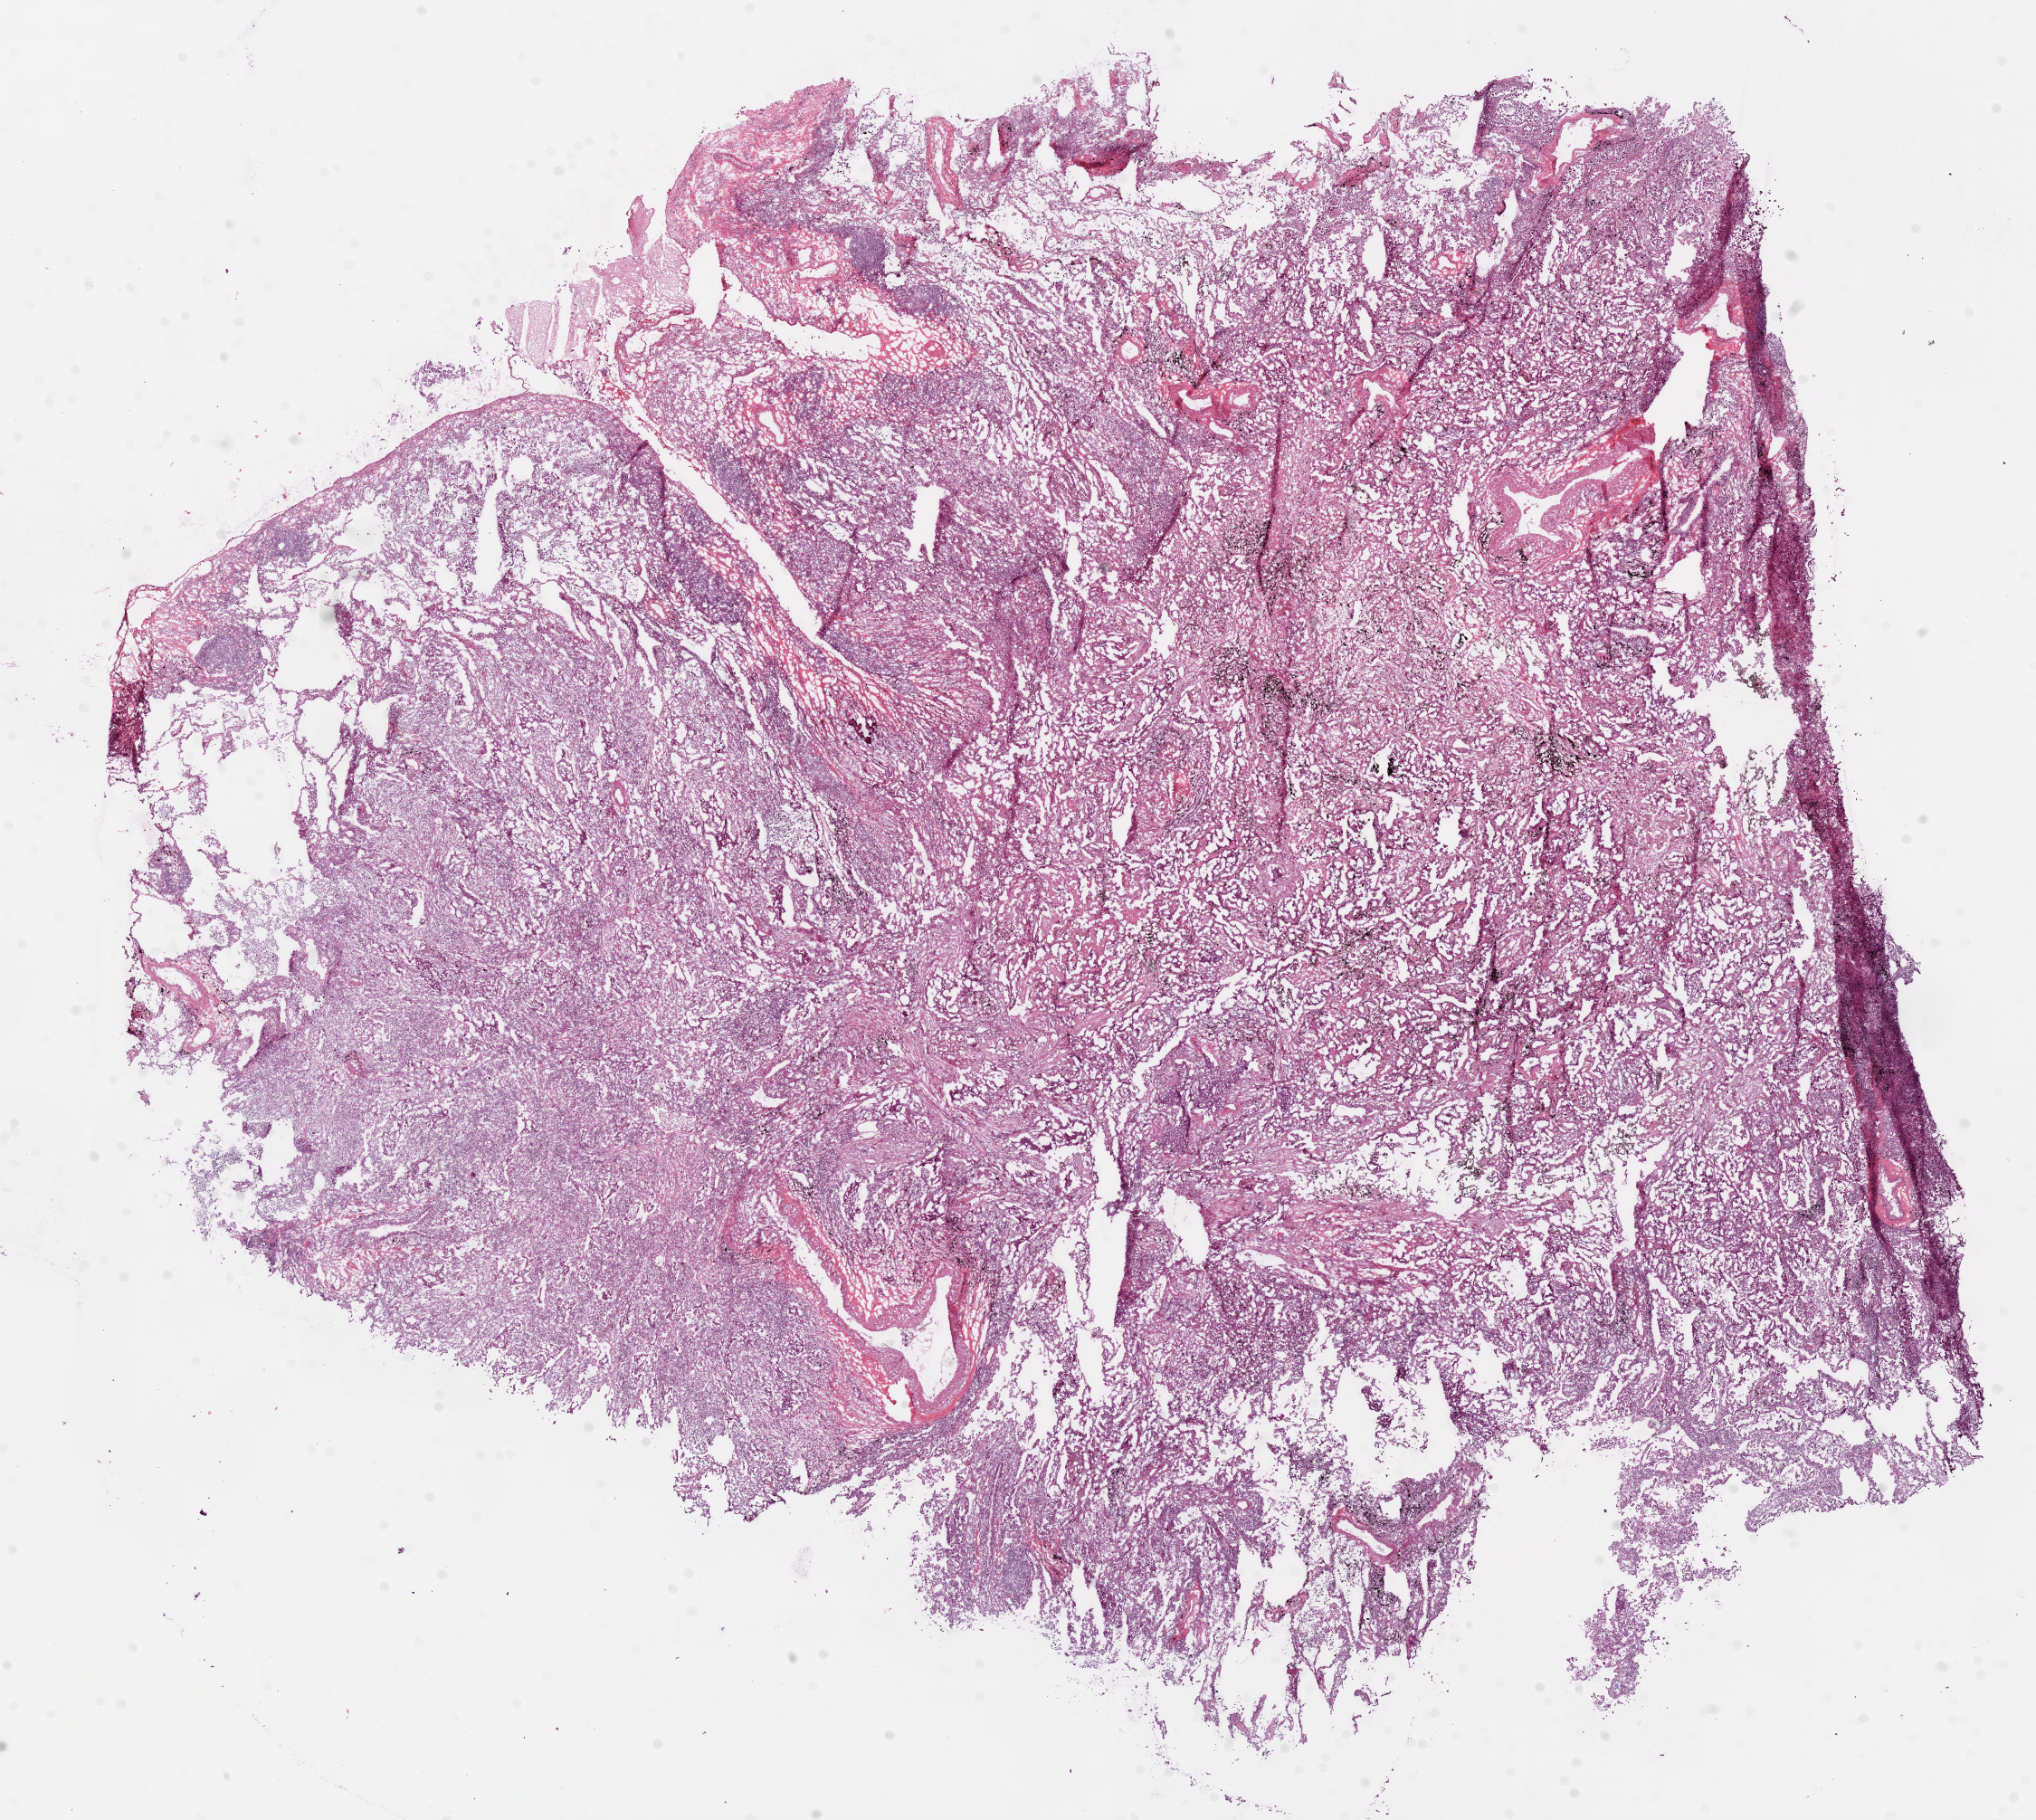
Whole-slide histology image, H&E-stained — low-resolution overview of the scanned area, about 18.1 x 16.1 mm (from a 20x scan). Frozen section from the top of the tissue portion. Primary tumour sample from the lung. Female, age 57 years at initial diagnosis. Pathologist review of this section (percent, as recorded): tumour cells 50%, tumour nuclei 65%, normal cells 20%, stromal cells 30%, necrosis 0%.
* diagnosis: Adenocarcinoma, NOS
* laterality: right